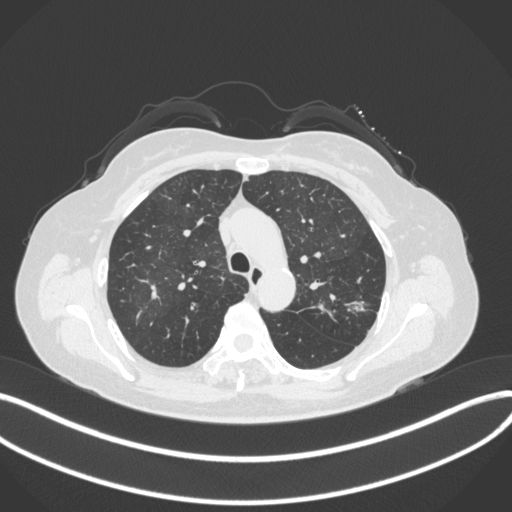
Chest CT, one axial slice. Position 250 of 330 along the scan axis. Reconstruction kernel B31f. 120 kVp. Lung window (W 1500 / L -600 HU). 1 mm slice thickness. 512 × 512 image matrix. Patient: female, 60 years. Case-level facts recorded for this patient, not image findings: clinical TNM (as recorded): T1c N0 M0.
Annotated regions visible in this slice (rectangle marked by the reading radiologist):
- lung tumour (recorded histology: adenocarcinoma): bounding box <342,297,368,316> (left, top, right, bottom; pixels)